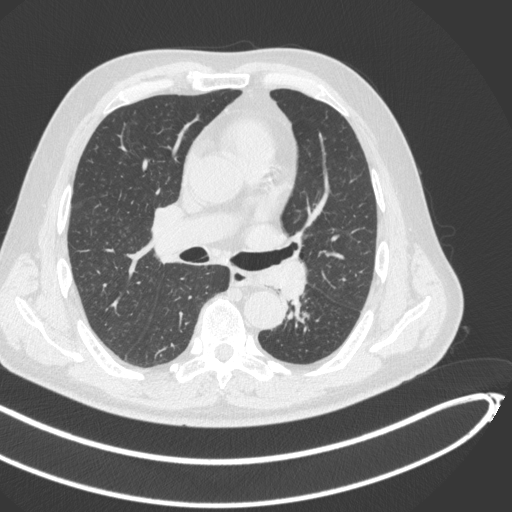
Chest CT, one axial slice; slice 268 of 466 in the series (ordered by position); reconstruction kernel B31f; 120 kVp; lung window (W 1500 / L -600 HU); 512 × 512 image matrix. Patient: male, 64 years. Case-level facts recorded for this patient, not image findings: clinical TNM (as recorded): T1c N0 M0; histopathological grade: G2.
Structures marked on this image (bounding box drawn by a radiologist):
- lung tumour (recorded histology: squamous cell carcinoma): bounding box (x1, y1, x2, y2) in pixels: (259, 264, 312, 309)